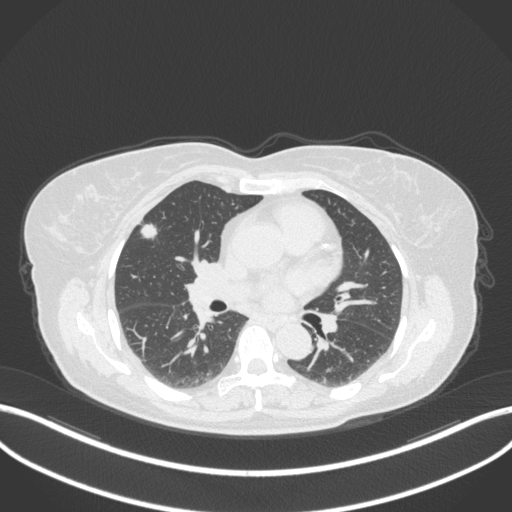
Chest CT, one axial slice; slice 181 of 310 in the series (ordered by position); reconstruction kernel B31f; 120 kVp; lung window (W 1500 / L -600 HU); 512 × 512 image matrix, field of view 400 × 400 mm. Patient: female, 55 years. From the clinical record (not read from this slice): clinical TNM (as recorded): T1b N0 M0.
Structures marked on this image (rectangle marked by the reading radiologist):
- lung tumour (recorded histology: adenocarcinoma): bounding box (x1, y1, x2, y2) in pixels: (134, 218, 158, 244)